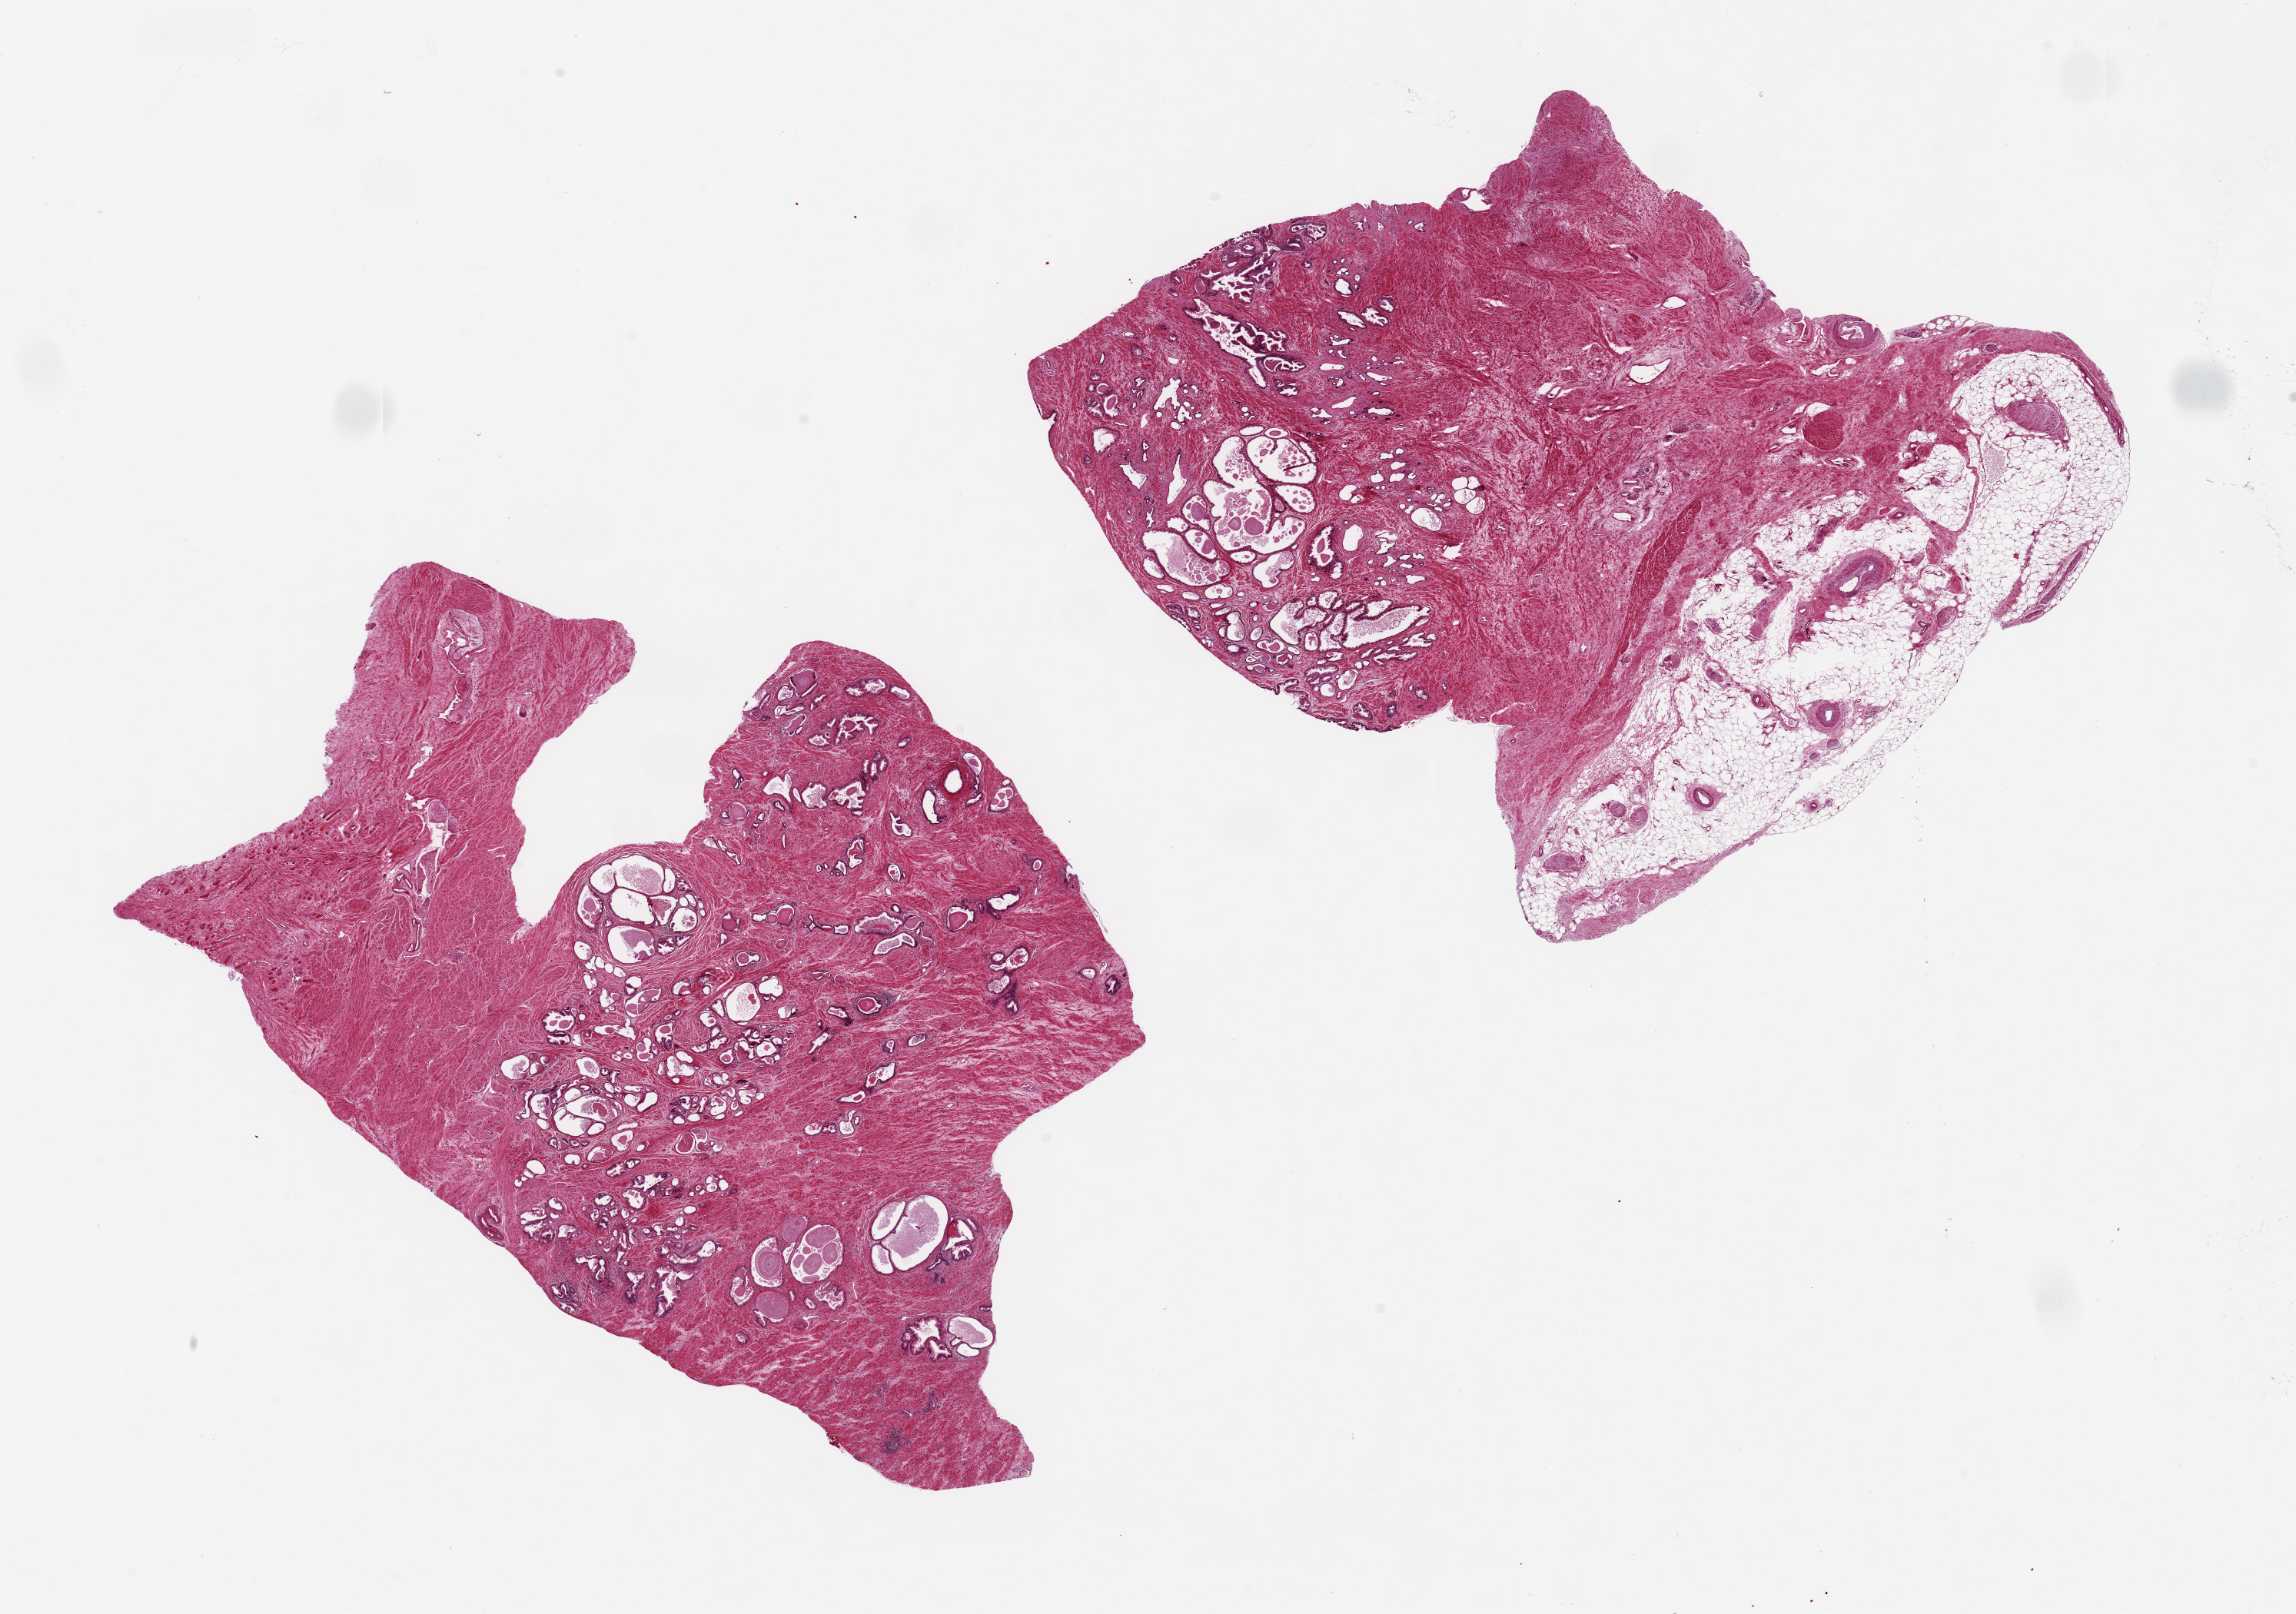
Haematoxylin and eosin whole-slide image — a low-resolution overview of the entire scanned area, about 23.6 x 16.6 mm, PAXgene-fixed, paraffin-embedded tissue, sampled site (target tissue): prostate, donor tissue sample. Donor: male.
Reviewer comment on this tissue sample: 2 pieces 9x7 & 8x7 mm; hyperplasia; one piece with ~30% adipose7on one side.